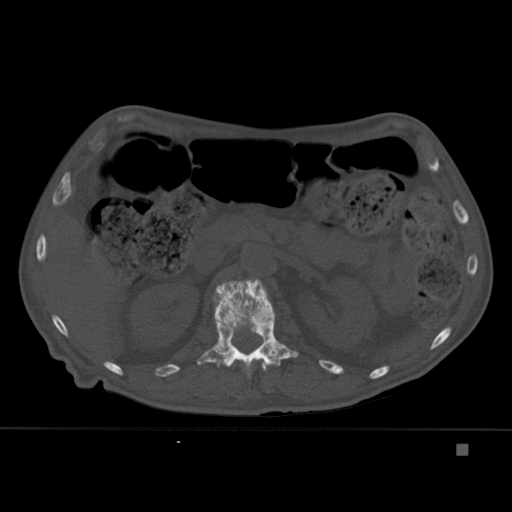
CT including the spine, one axial slice; bone window (W 1800 / L 400 HU); 512 × 512 image matrix, field of view 378 × 378 mm. Male patient, age 75 years. Case-level facts recorded for this patient, not image findings: primary cancer: prostate.
Outlined on this slice (semi-automatically segmented with operator editing):
- L1 vertebra: bounding box [x1, y1, x2, y2] px = [197, 279, 299, 376]
- T12 vertebra: [233, 359, 267, 371]